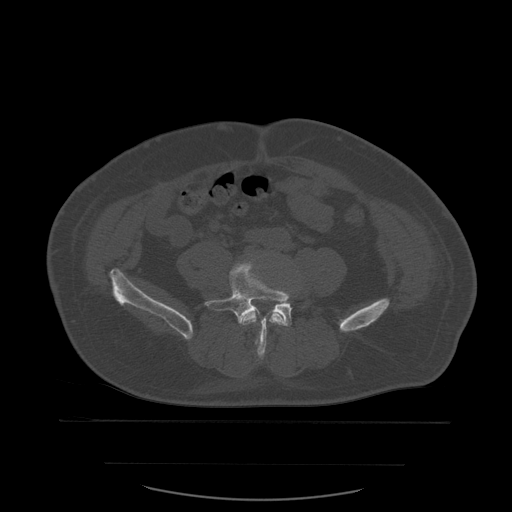
CT including the spine, one axial slice. Position 147 of 590 along the scan axis. Bone window (W 1800 / L 400 HU). 1.25 mm slice thickness. 512 × 512 image matrix, field of view 479 × 479 mm. Patient age 71 years. Case-level facts recorded for this patient, not image findings: primary cancer: lung; vertebrae with lytic lesions (as recorded): T1, T2, L5, S1.
Outlined on this slice (semi-automatically segmented with operator editing):
- L4 vertebra: bounding box (x1, y1, x2, y2) in pixels: (242, 311, 285, 345)
- L5 vertebra: (205, 262, 292, 359)